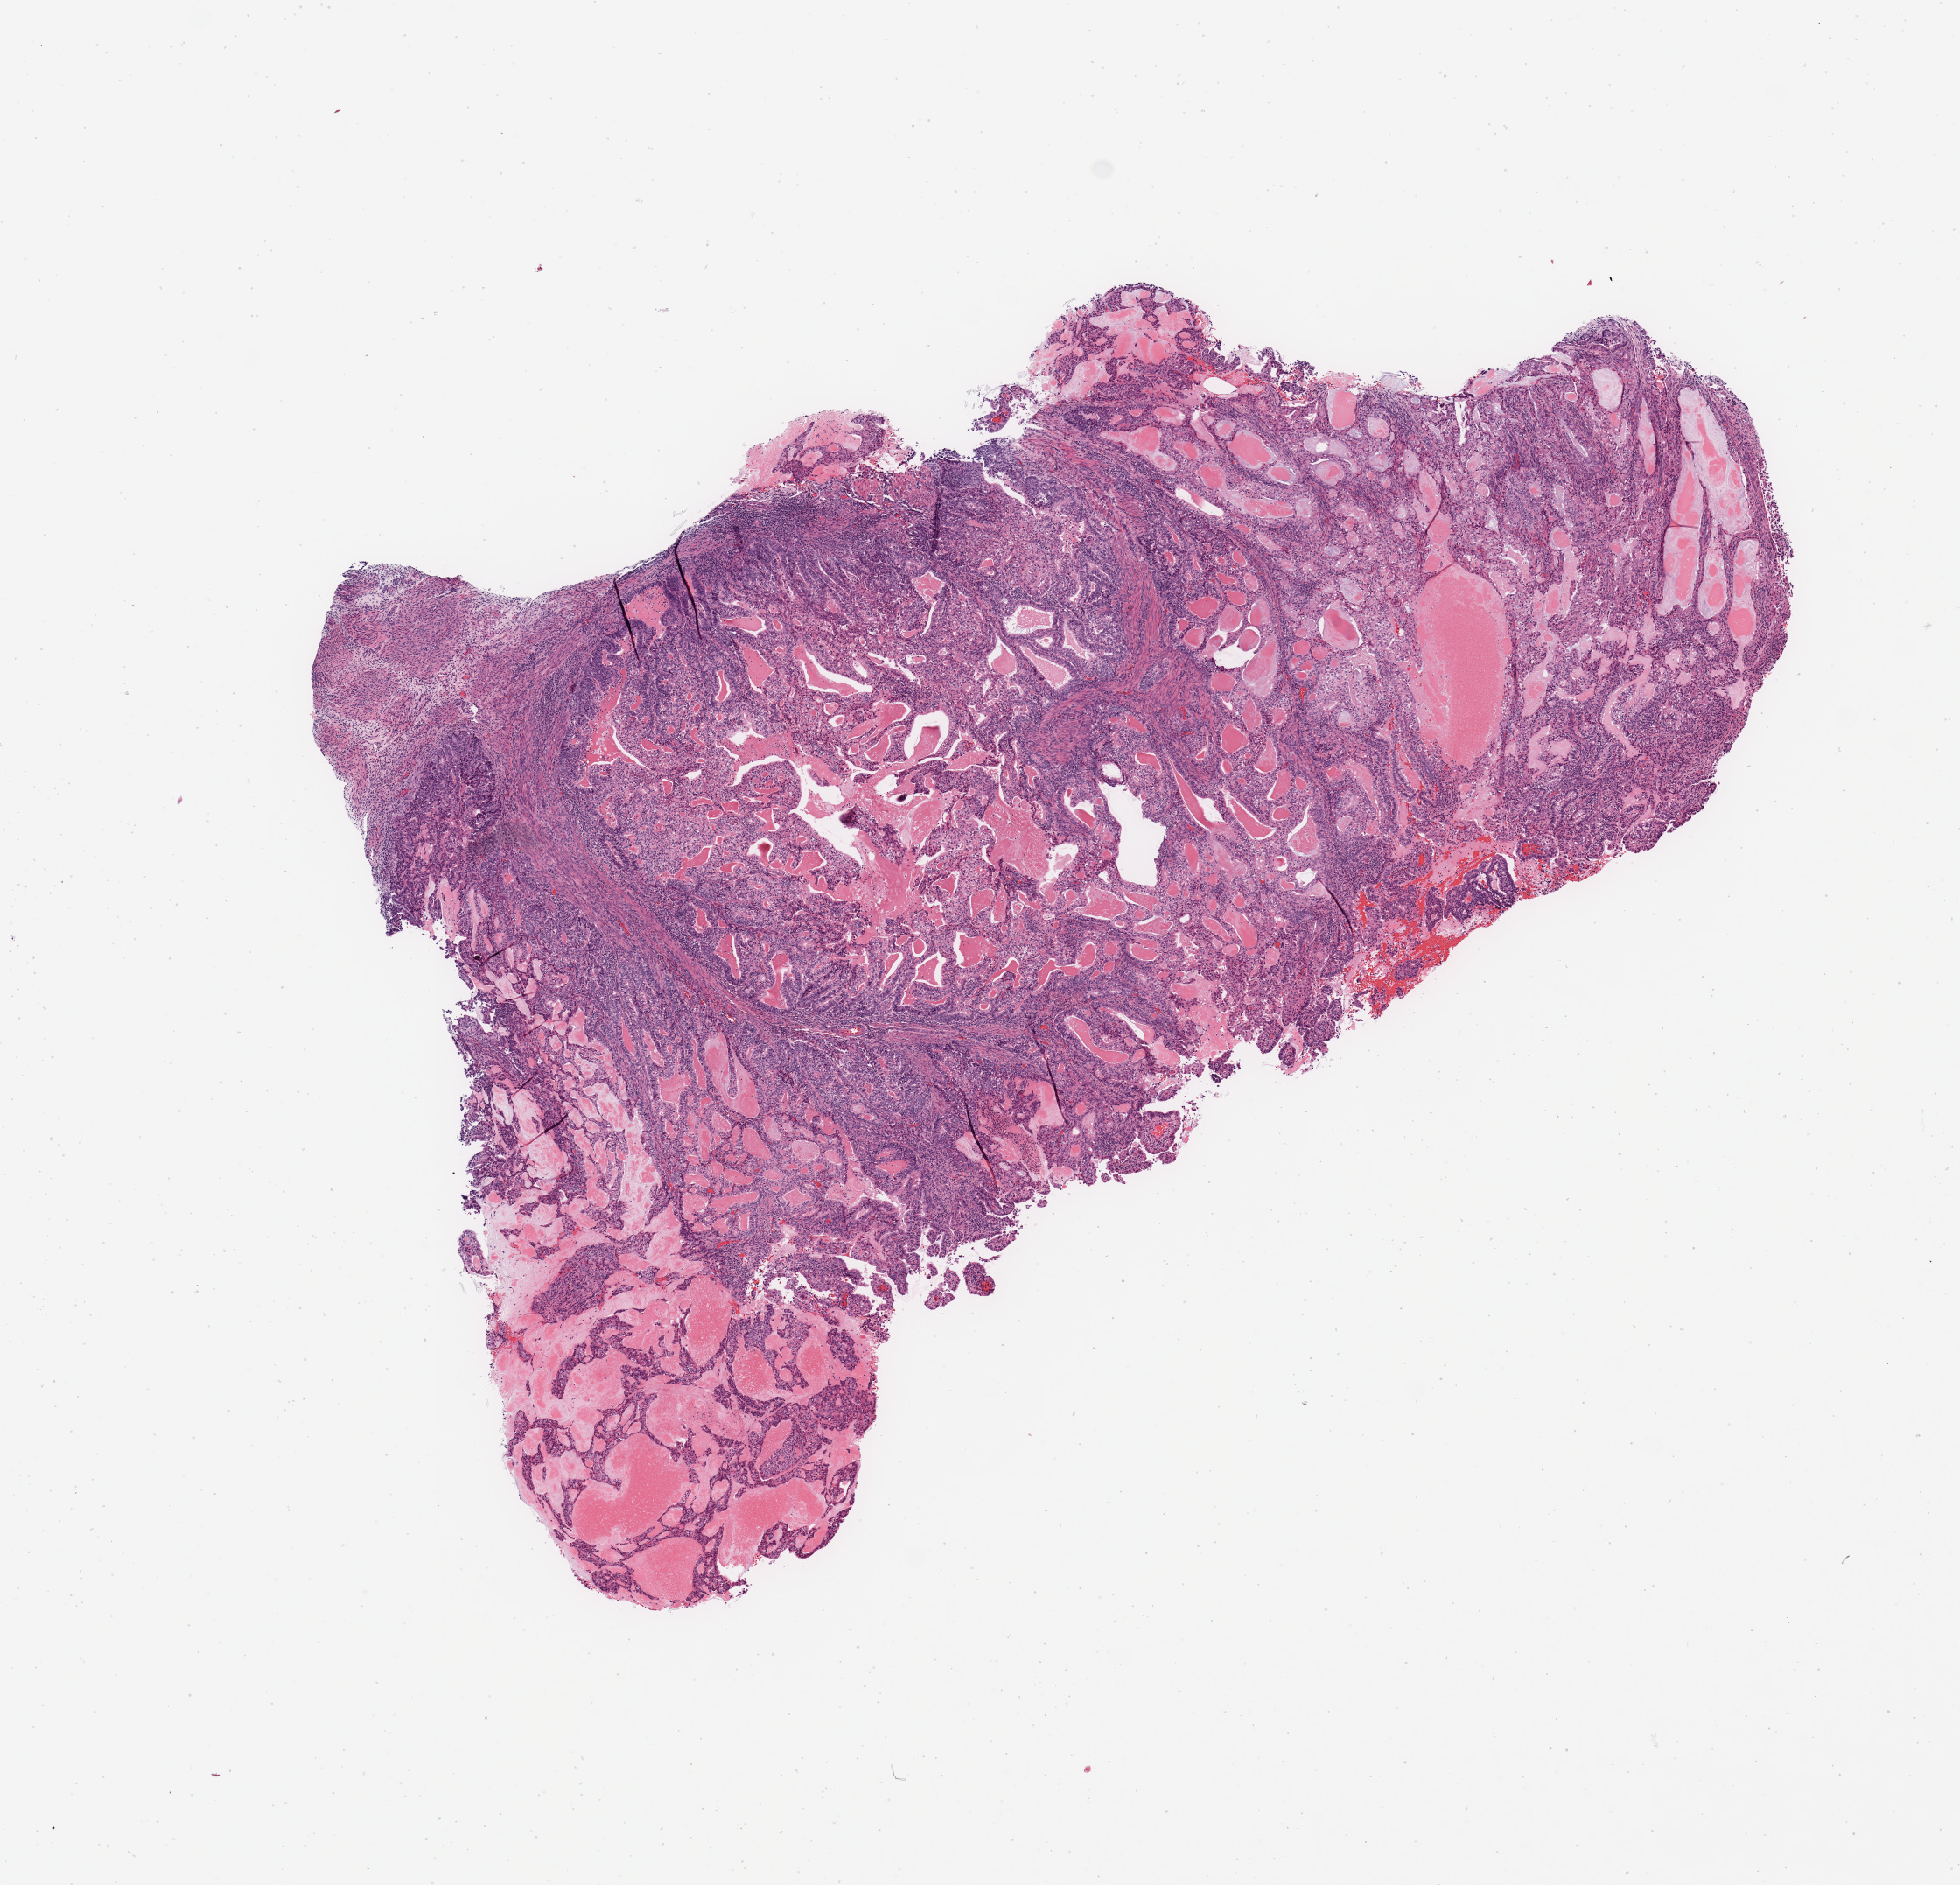
H&E whole-slide image, a low-resolution overview of the entire scanned area, about 8.9 x 8.5 mm (acquisition: 20x scan). Tumour tissue sample, uterus. 62-year-old female patient. Histologic grade: G2 (moderately differentiated).
* diagnosis: Endometrioid adenocarcinoma, NOS
* AJCC pathologic stage: I